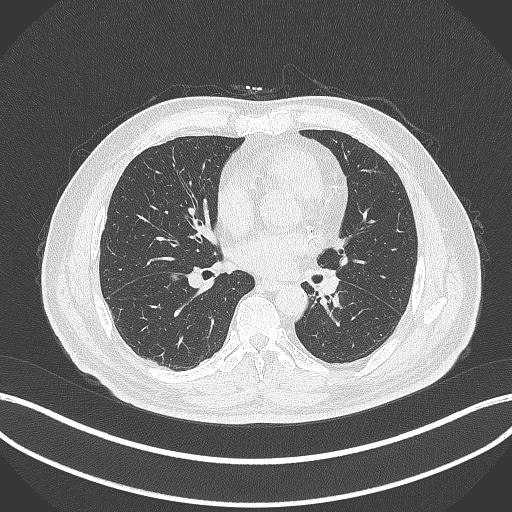
Chest CT, one axial slice. Slice 133 of 312 in the series (ordered by position). Reconstruction kernel B70f. 120 kVp. Lung window (W 1500 / L -600 HU). 1 mm slice thickness. 512 × 512 image matrix, field of view 400 × 400 mm. Male patient, age 71 years. Case-level facts recorded for this patient, not image findings: clinical TNM (as recorded): T1b N0 M0.
Structures marked on this image (bounding box drawn by a radiologist):
- lung tumour (recorded histology: squamous cell carcinoma): bounding box [x1, y1, x2, y2] px = [315, 268, 346, 300]